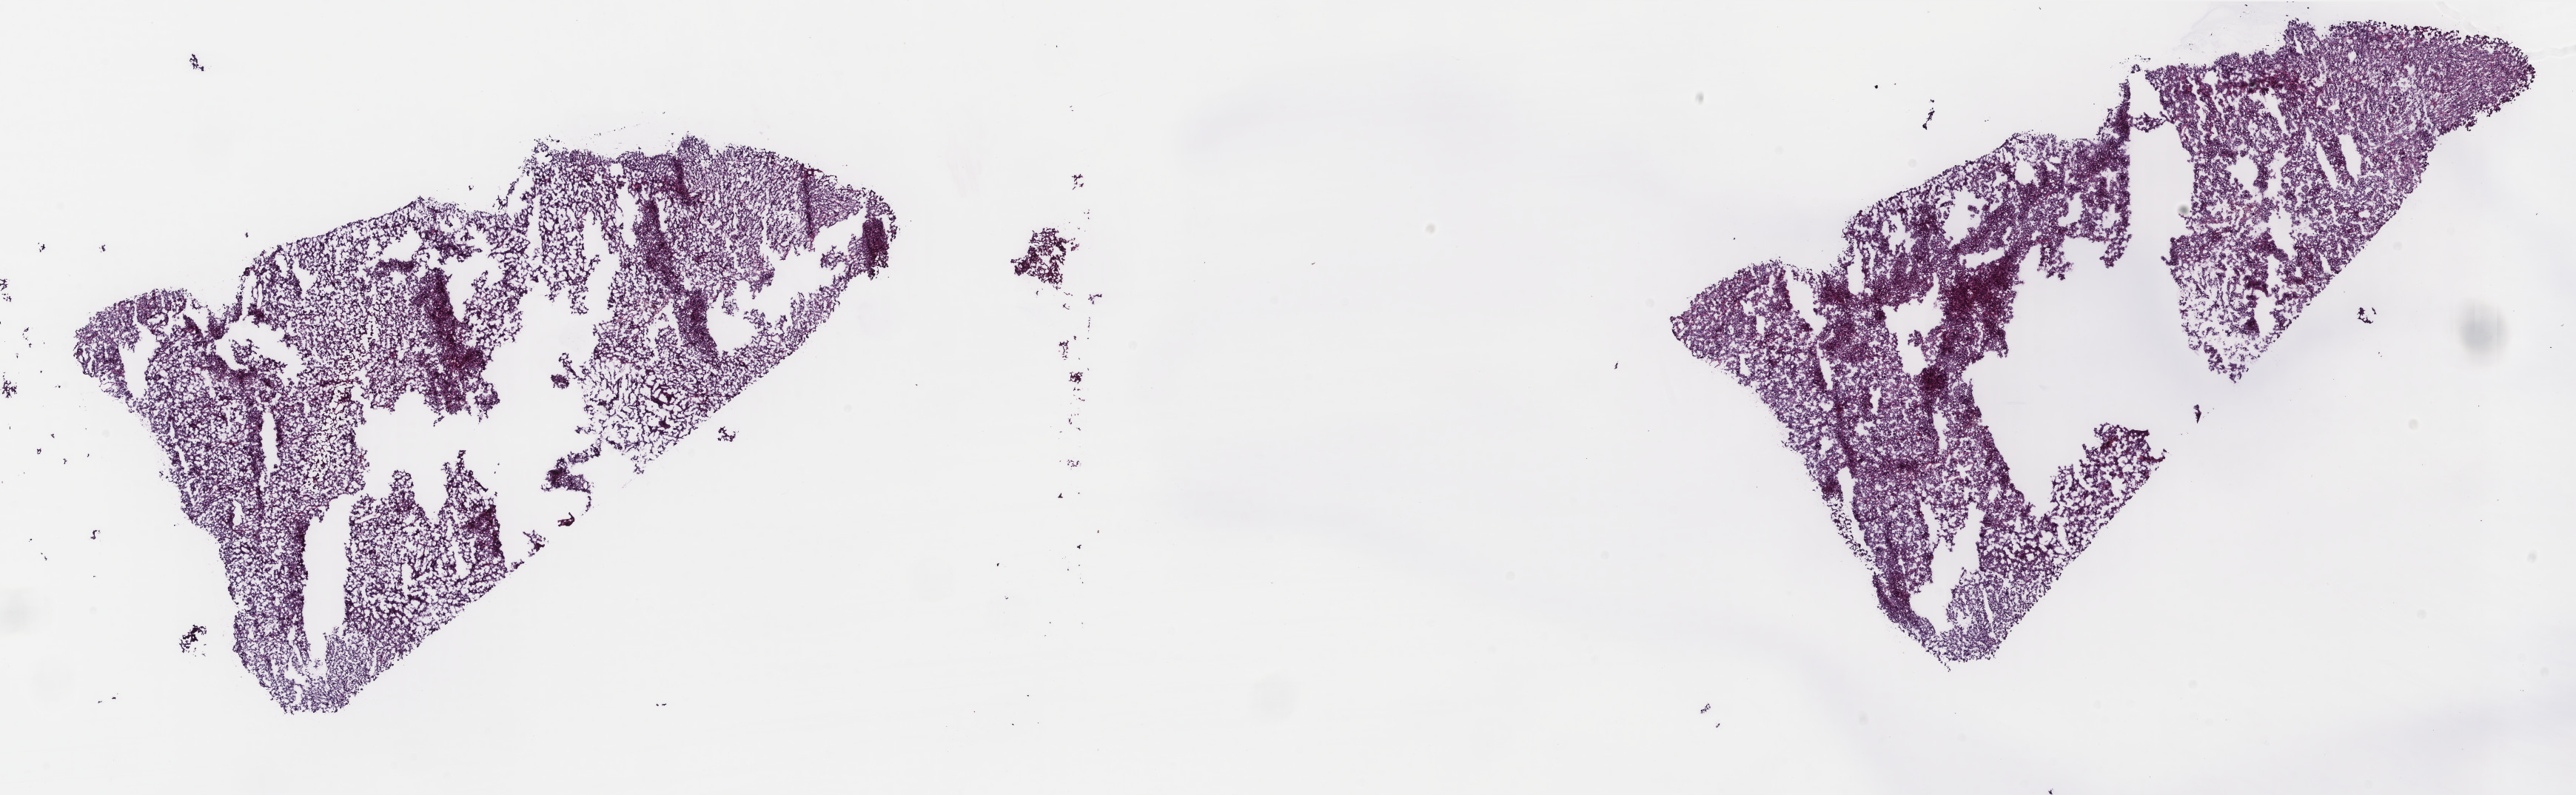
Digitized H&E tissue section (whole slide) — shown as a low-resolution overview of the whole scanned area (about 27.6 x 8.5 mm, from a 40x scan); frozen section from the top of the tissue portion; metastatic tumour sample, sampled site not recorded. Female, age 83 years at initial diagnosis. Composition of this section per pathologist review: tumour cells 90%, tumour nuclei 90%, normal cells 0%, stromal cells 10%, necrosis 0%. Infiltration values recorded for this section: lymphocyte infiltration 2%, monocyte infiltration 1%, neutrophil infiltration 0%.
This section: metastatic tumour tissue. Patient diagnosis: Malignant melanoma, NOS.